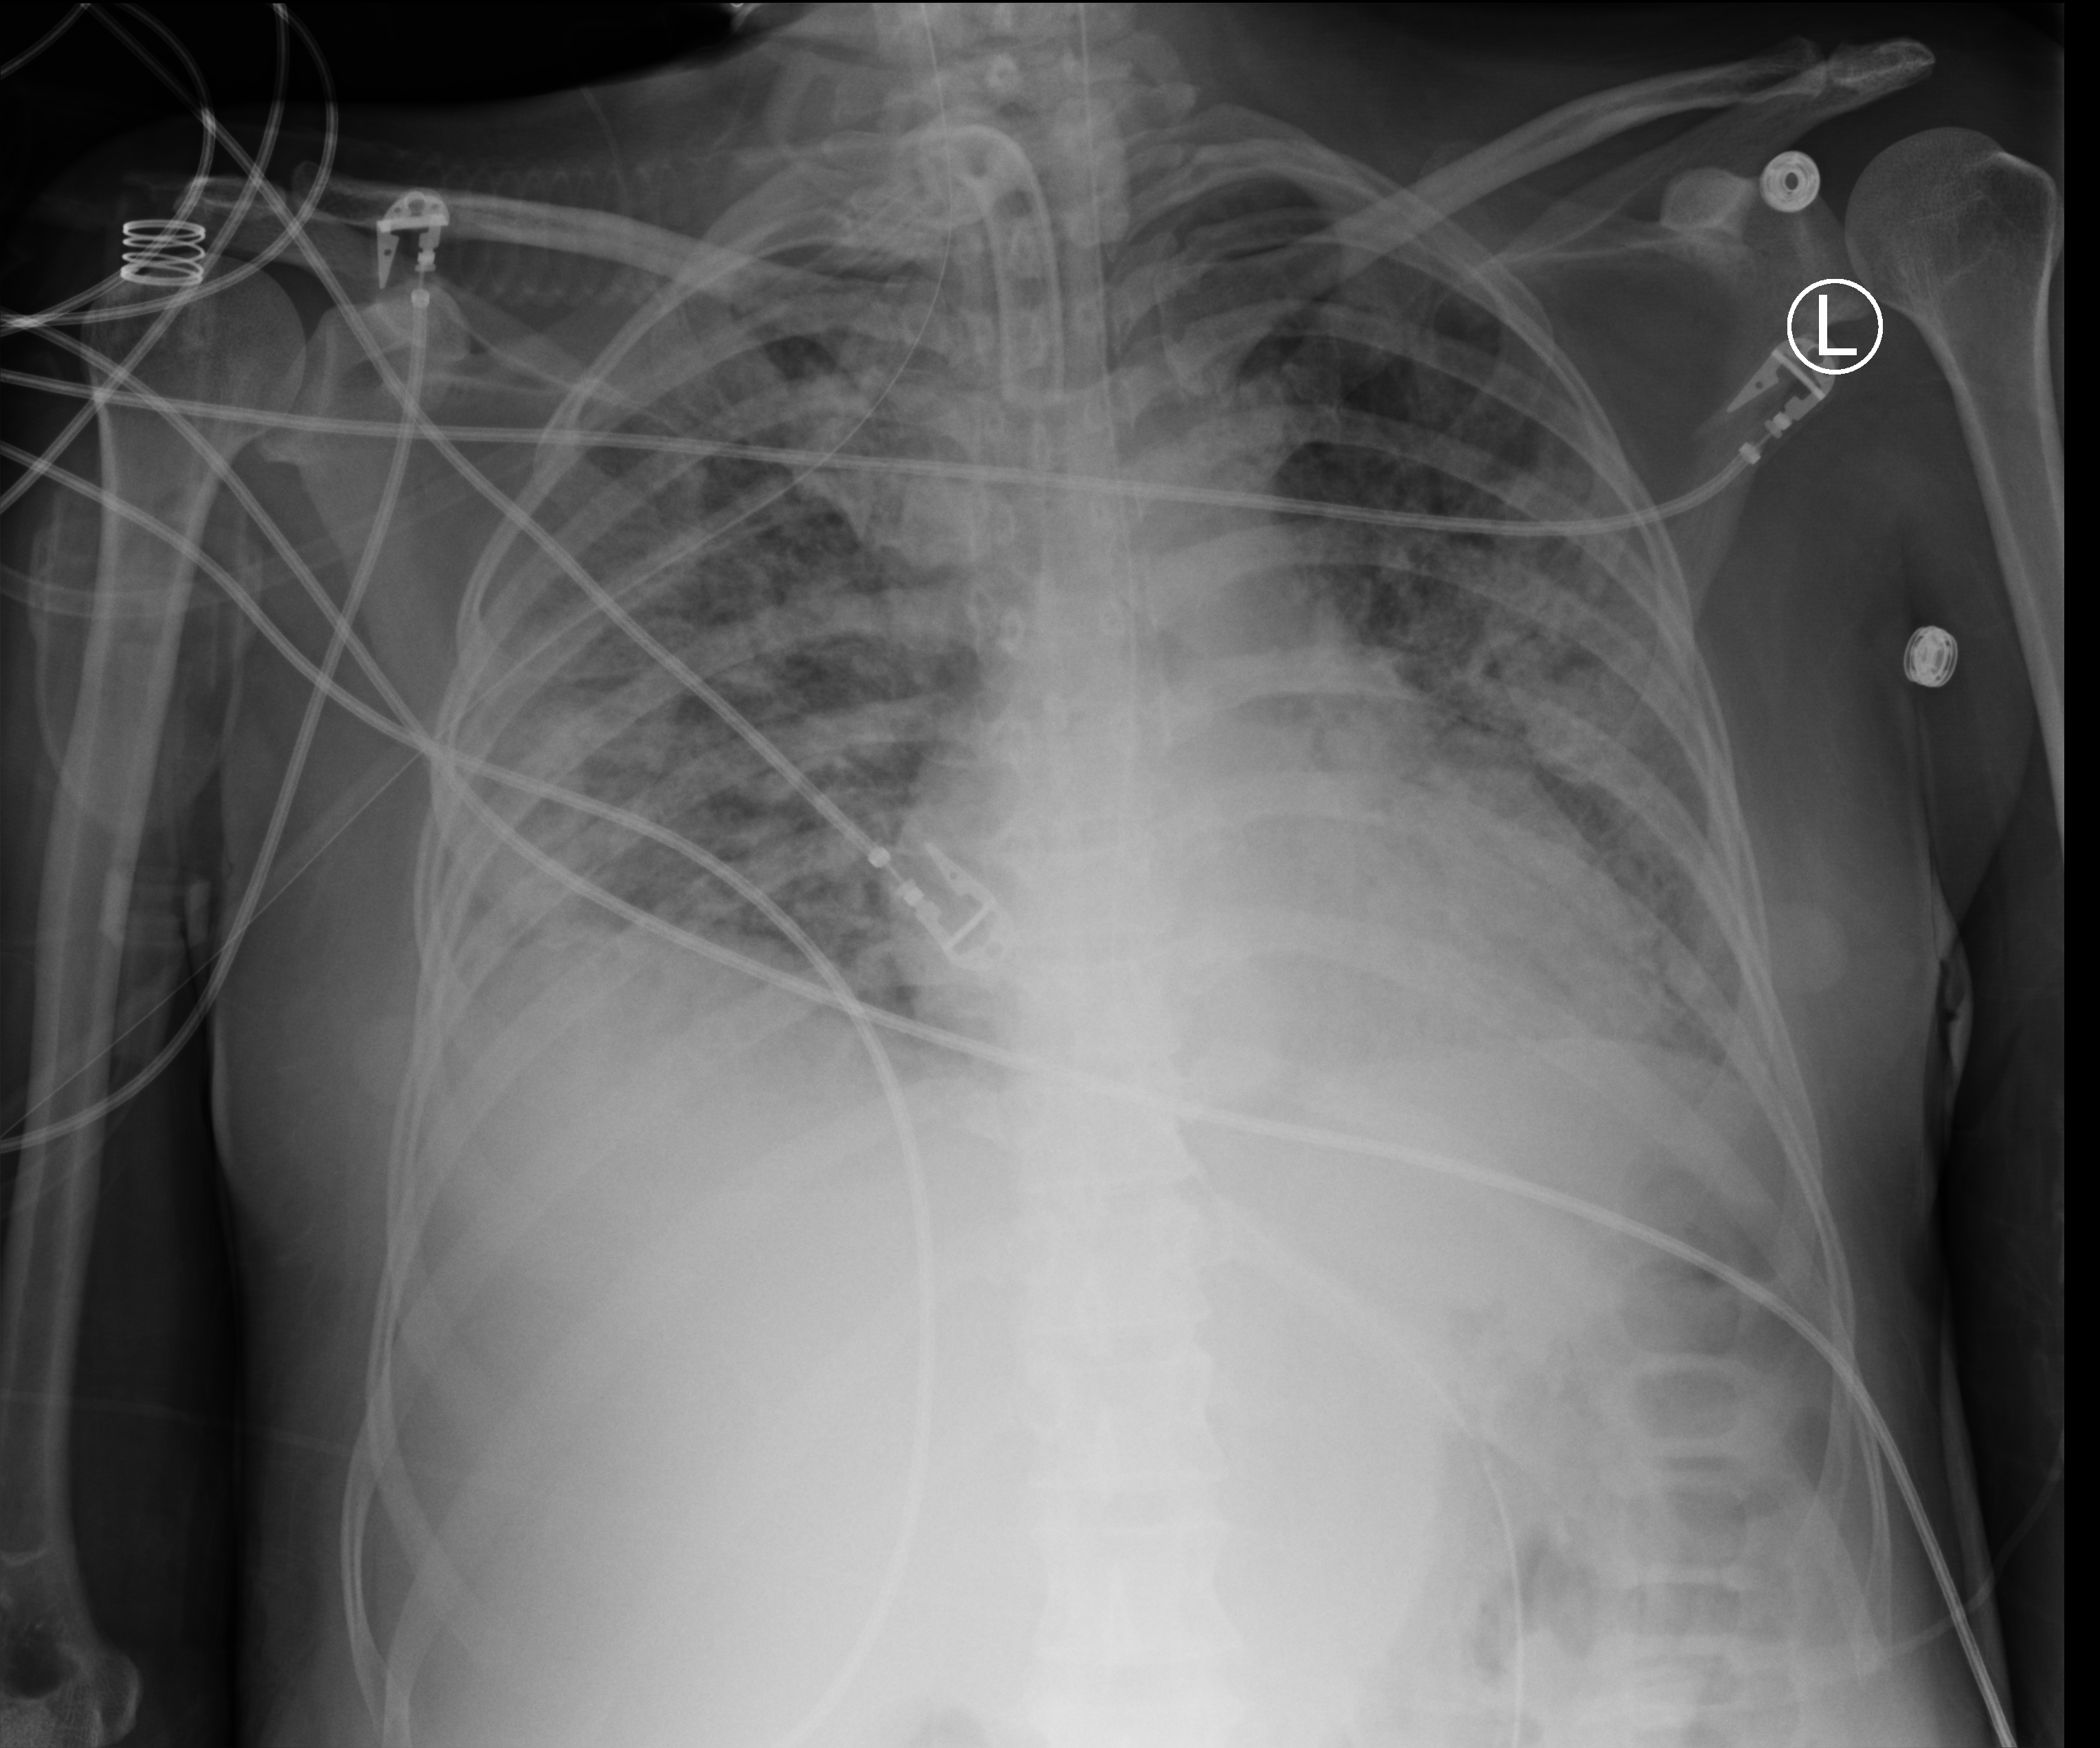
Portable chest radiograph. Female patient hospitalised with COVID-19, age 18–59 years.
From the hospital-stay record, not from the radiograph (when in the stay this image was taken is not recorded):
- diabetes (admission record): no